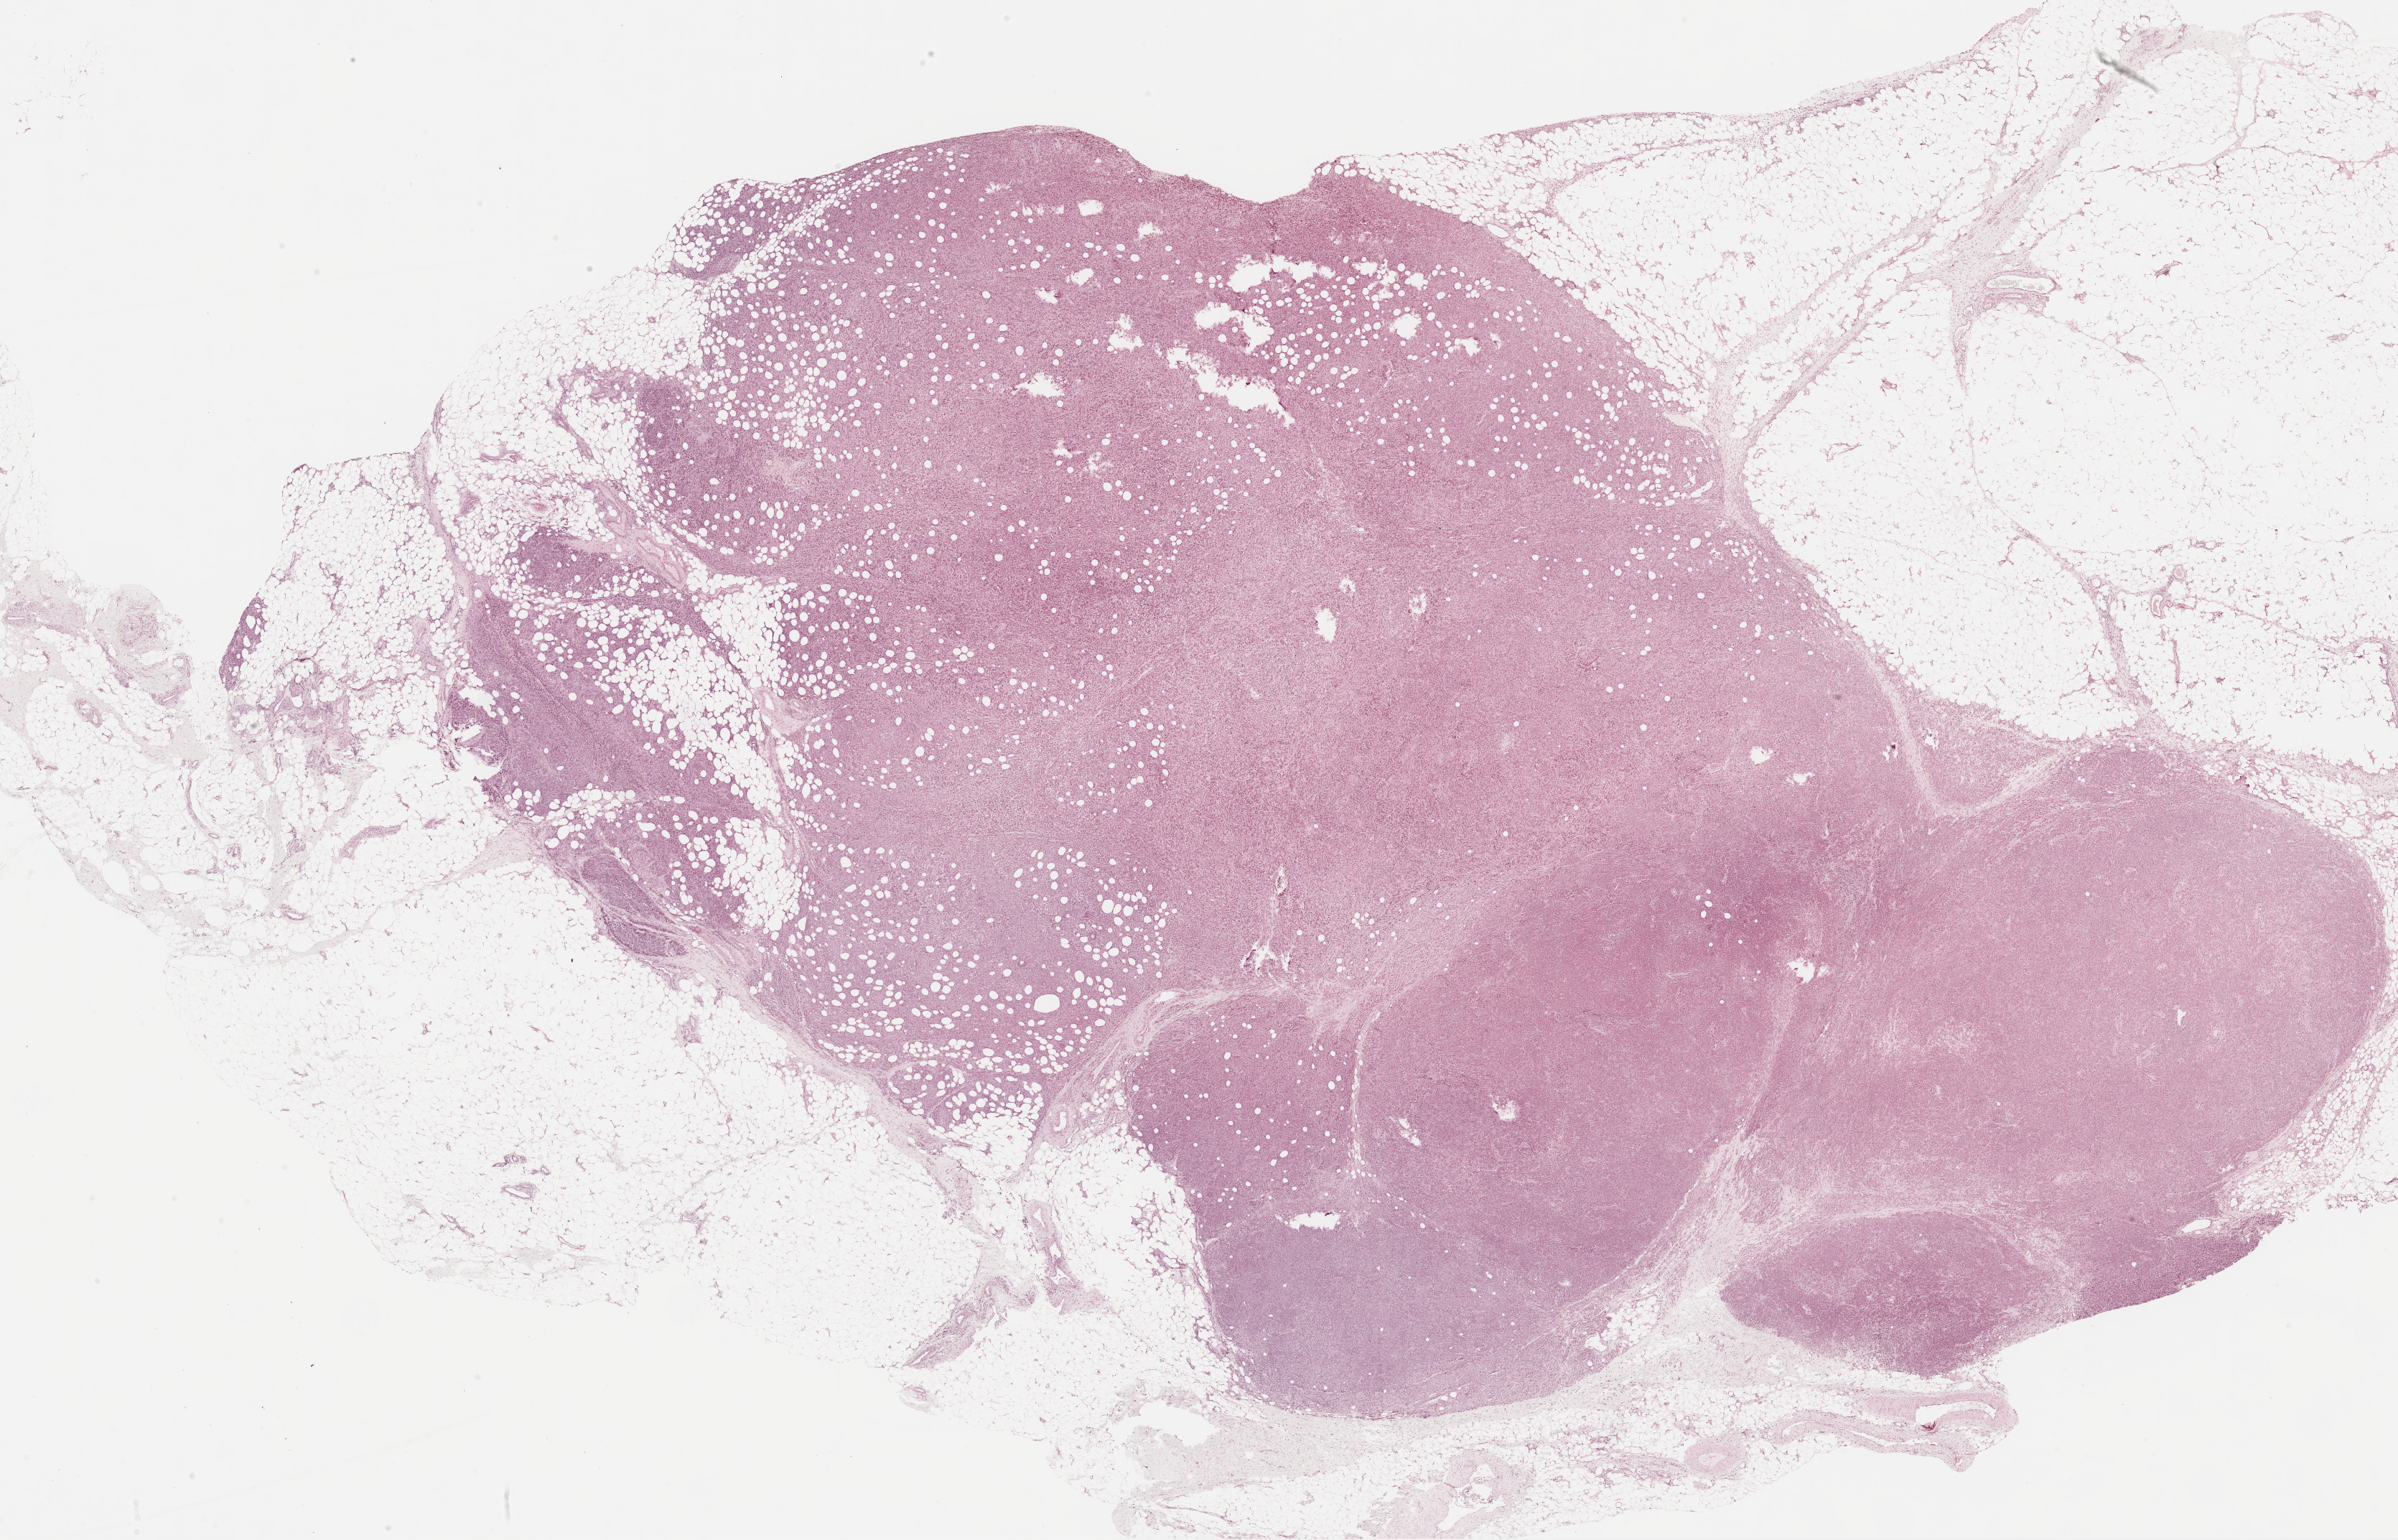
Hematoxylin and eosin (H&E) stained whole-slide image — shown as a low-resolution overview of the whole scanned area (about 26.9 x 17.3 mm, slide scanned at 20x). FFPE section. Metastatic tumour sample. Female patient; age at initial diagnosis 54 years.
- this section: metastatic tumour tissue
- patient diagnosis: Malignant melanoma, NOS